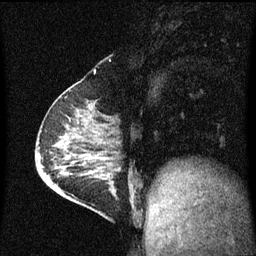
Breast MRI (dynamic contrast-enhanced), one sagittal slice; slice 24 of 60 in the series (ordered by position); dynamic contrast-enhanced series, image 2 of 3 at this slice position (ordered by acquisition); 1.5 T; TE 4.2 ms, TR 8 ms; 256 × 256 image matrix, field of view 200 × 200 mm. Female patient, age 64 years.
Outlined on this slice (semi-automatically segmented with operator editing):
- analysis volume of interest (the breast-tissue region the enhancement analysis was run in; not a lesion): box from (x=87, y=176) to (x=130, y=217) px
- tumour enhancement mask (voxels above the 70 % enhancement threshold inside the analysis volume of interest): (x=94, y=176)–(x=113, y=187)